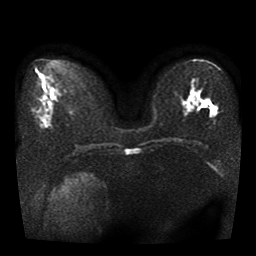
Breast MRI, one axial slice; slice 19 of 41 in the series (ordered by position); diffusion-weighted series; image 2 of 4 stored at this slice position (different b-values; order by instance number); 1.5 T; 5 mm slice thickness; 256 × 256 image matrix, field of view 330 × 330 mm. Female patient.
Annotated regions visible in this slice (outlined manually by an expert reader):
- tumour on diffusion-weighted imaging: bounding box [x1, y1, x2, y2] px = [209, 103, 215, 108]